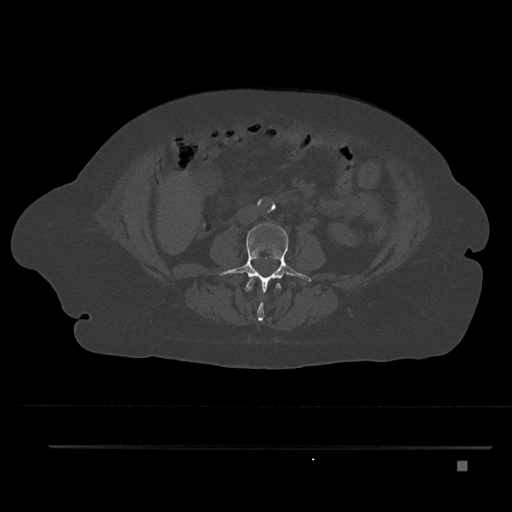
CT including the spine, one axial slice. Position 130 of 797 along the scan axis. Reconstruction kernel Br40s/3. Bone window (W 1800 / L 400 HU). 0.5 mm slice thickness. 512 × 512 image matrix, field of view 437 × 437 mm. Female patient, age 76 years. From the clinical record (not read from this slice): primary cancer: lung.
Outlined on this slice (semi-automatic segmentation, software-assisted and operator-edited):
- L2 vertebra: box from (x=245, y=279) to (x=282, y=322) px
- L3 vertebra: (x=219, y=222)–(x=311, y=292)